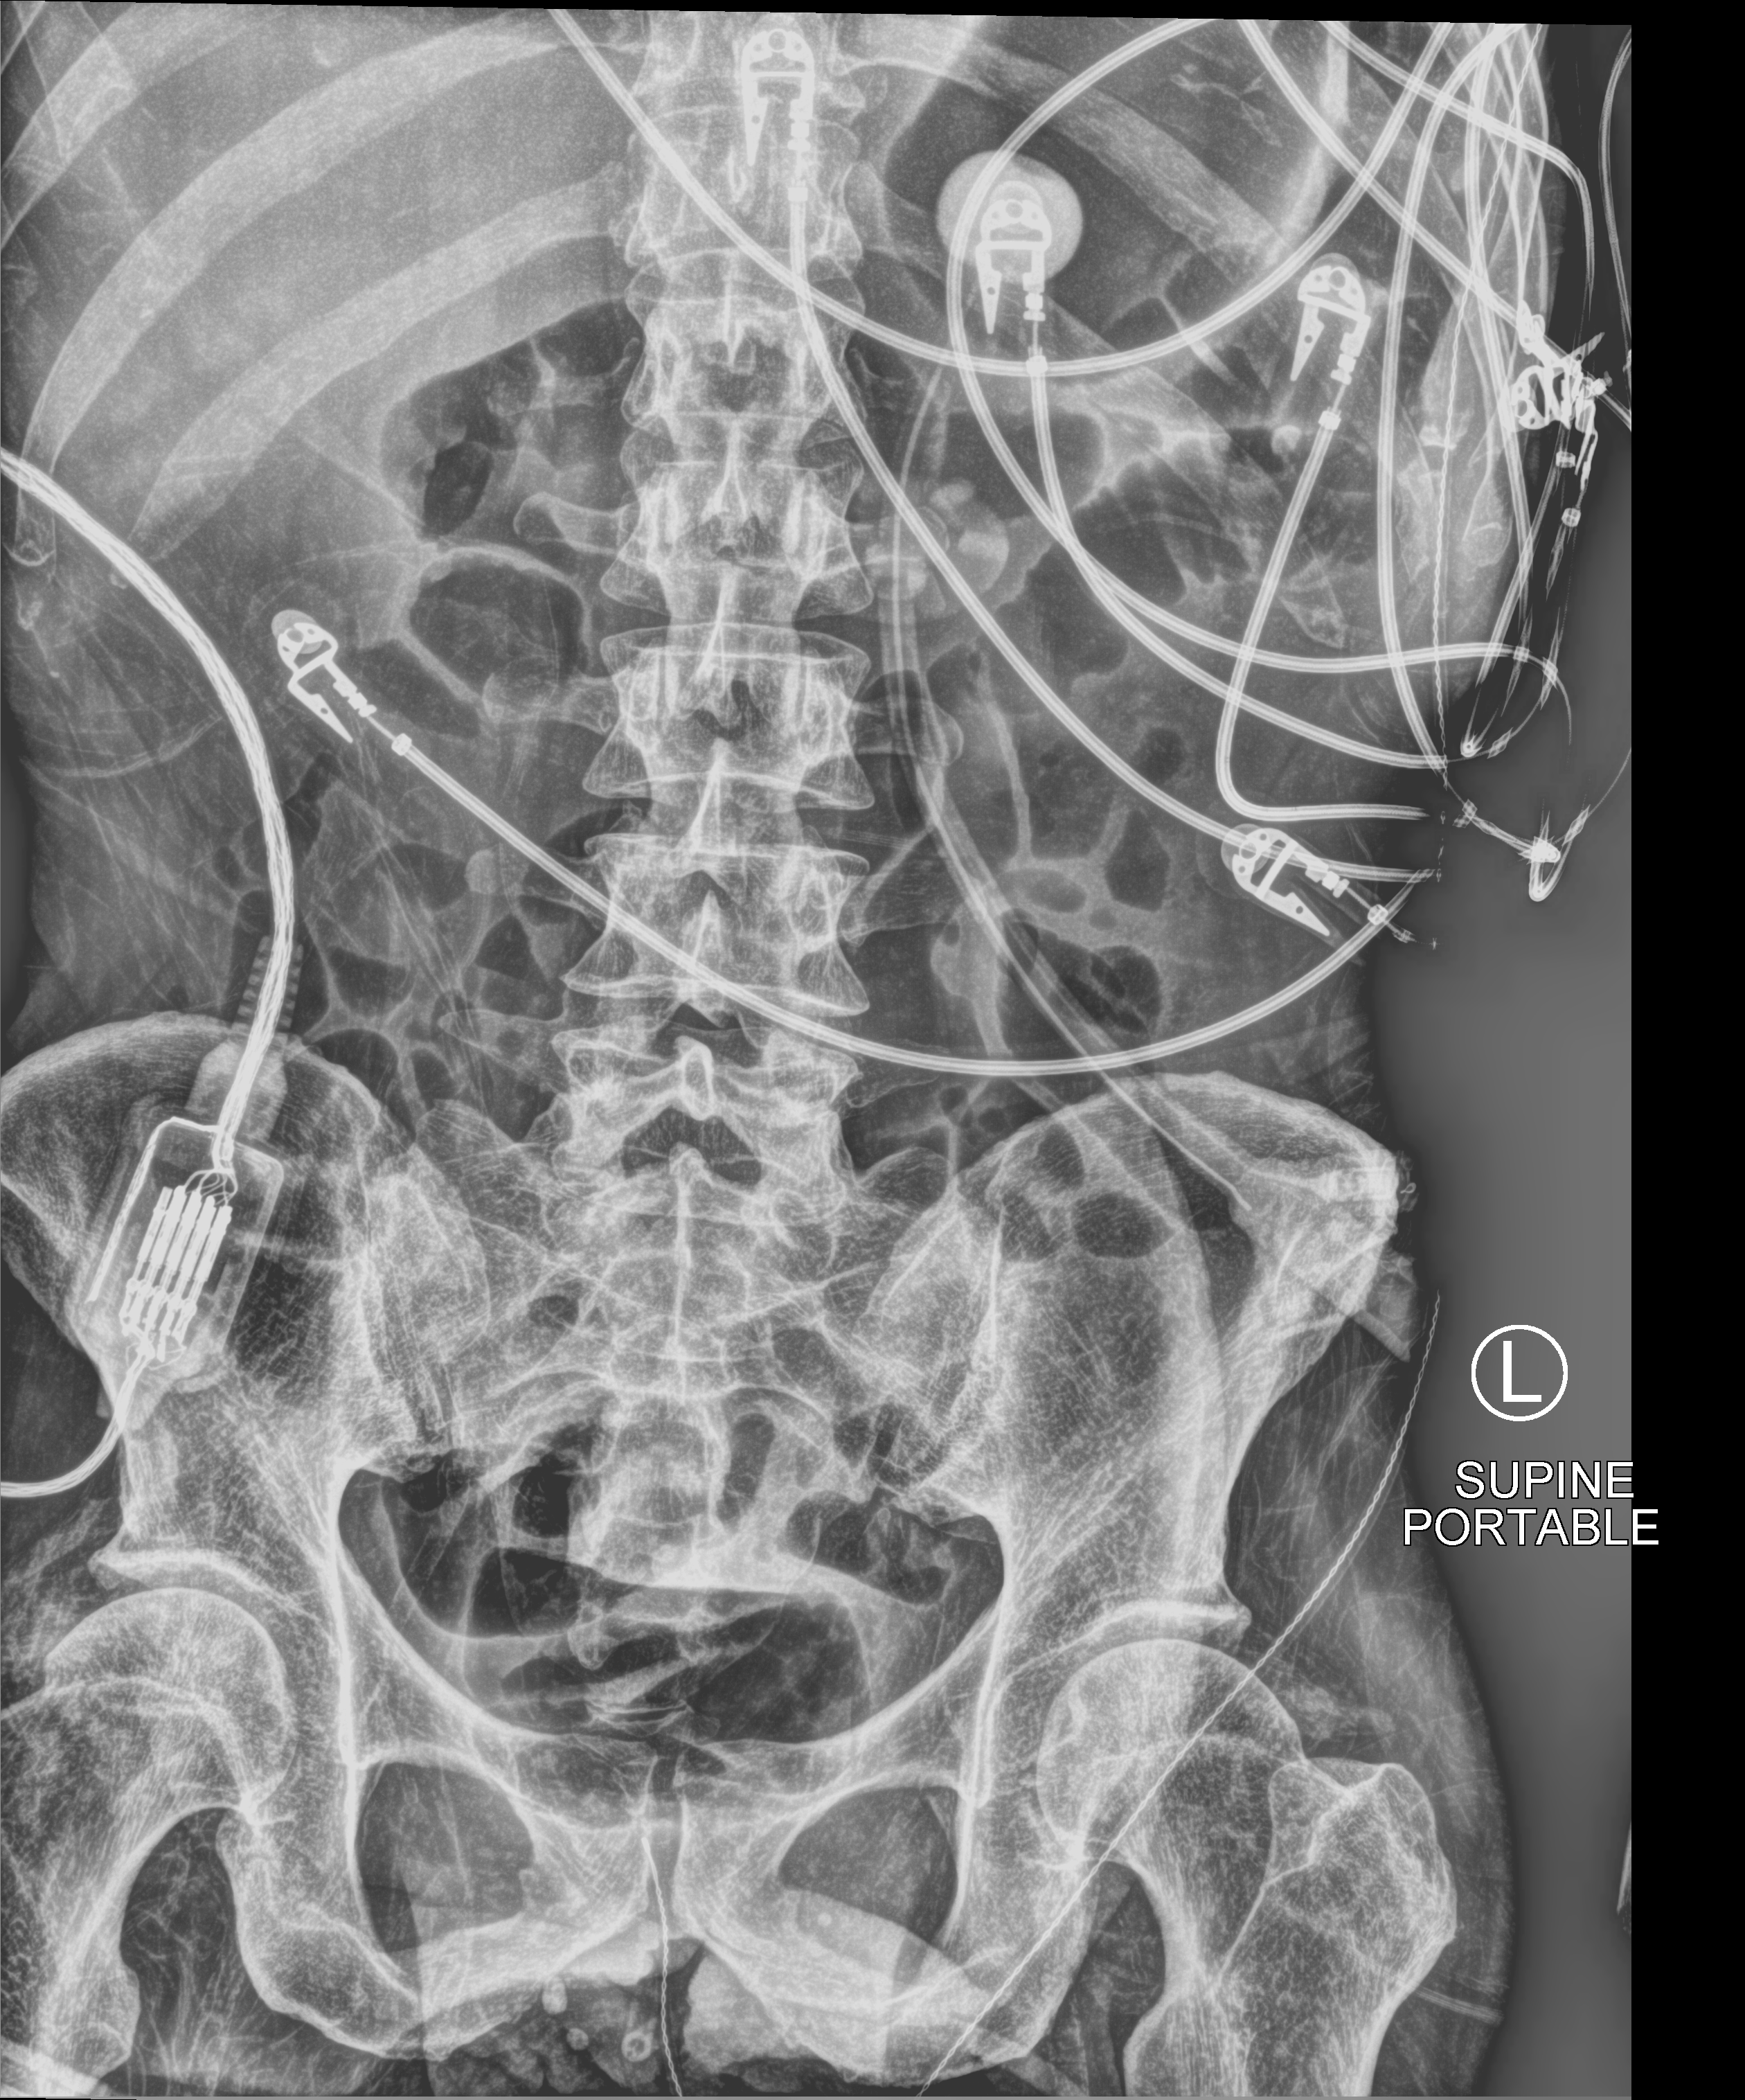
Bedside abdomen radiograph (computed radiography). Male patient hospitalised with COVID-19, age 18–59 years.
Admission-level facts for this patient (not findings on this image; timing relative to this image not recorded): admitted to intensive care during this hospital stay: yes; smoking status (admission record): never; length of hospital stay: 96 days.